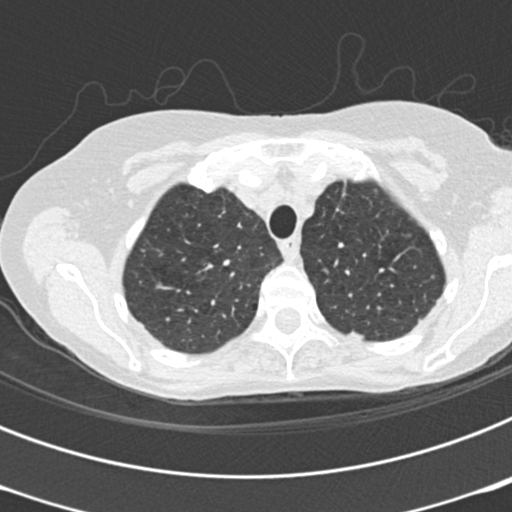
Low-dose screening chest CT, one axial slice; slice 169 of 199 in the series (ordered by position); reconstruction kernel B30f; lung window (W 1500 / L -600 HU); 2 mm slice thickness; 512 × 512 image matrix, field of view 290 × 290 mm.
Outlined on this slice (manually delineated by an expert):
- lesion 2 (nodule, upper lobe of left lung): bounding box (x1, y1, x2, y2) in pixels: (350, 332, 363, 339)